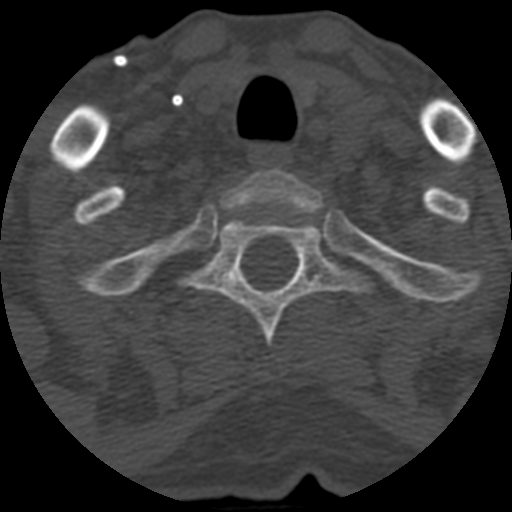
CT including the spine, one axial slice. Position 507 of 708 along the scan axis. Reconstruction kernel STANDARD. One of 3 acquisitions stored at this slice position. Bone window (W 1800 / L 400 HU). 1.25 mm slice thickness. 512 × 512 image matrix, field of view 160 × 160 mm. Patient age 55 years. From the clinical record (not read from this slice): primary cancer: colon.
Structures marked on this image (semi-automatic segmentation, software-assisted and operator-edited):
- T1 vertebra: bounding box <226,169,319,212> (left, top, right, bottom; pixels)
- T2 vertebra: <183,217,361,347>